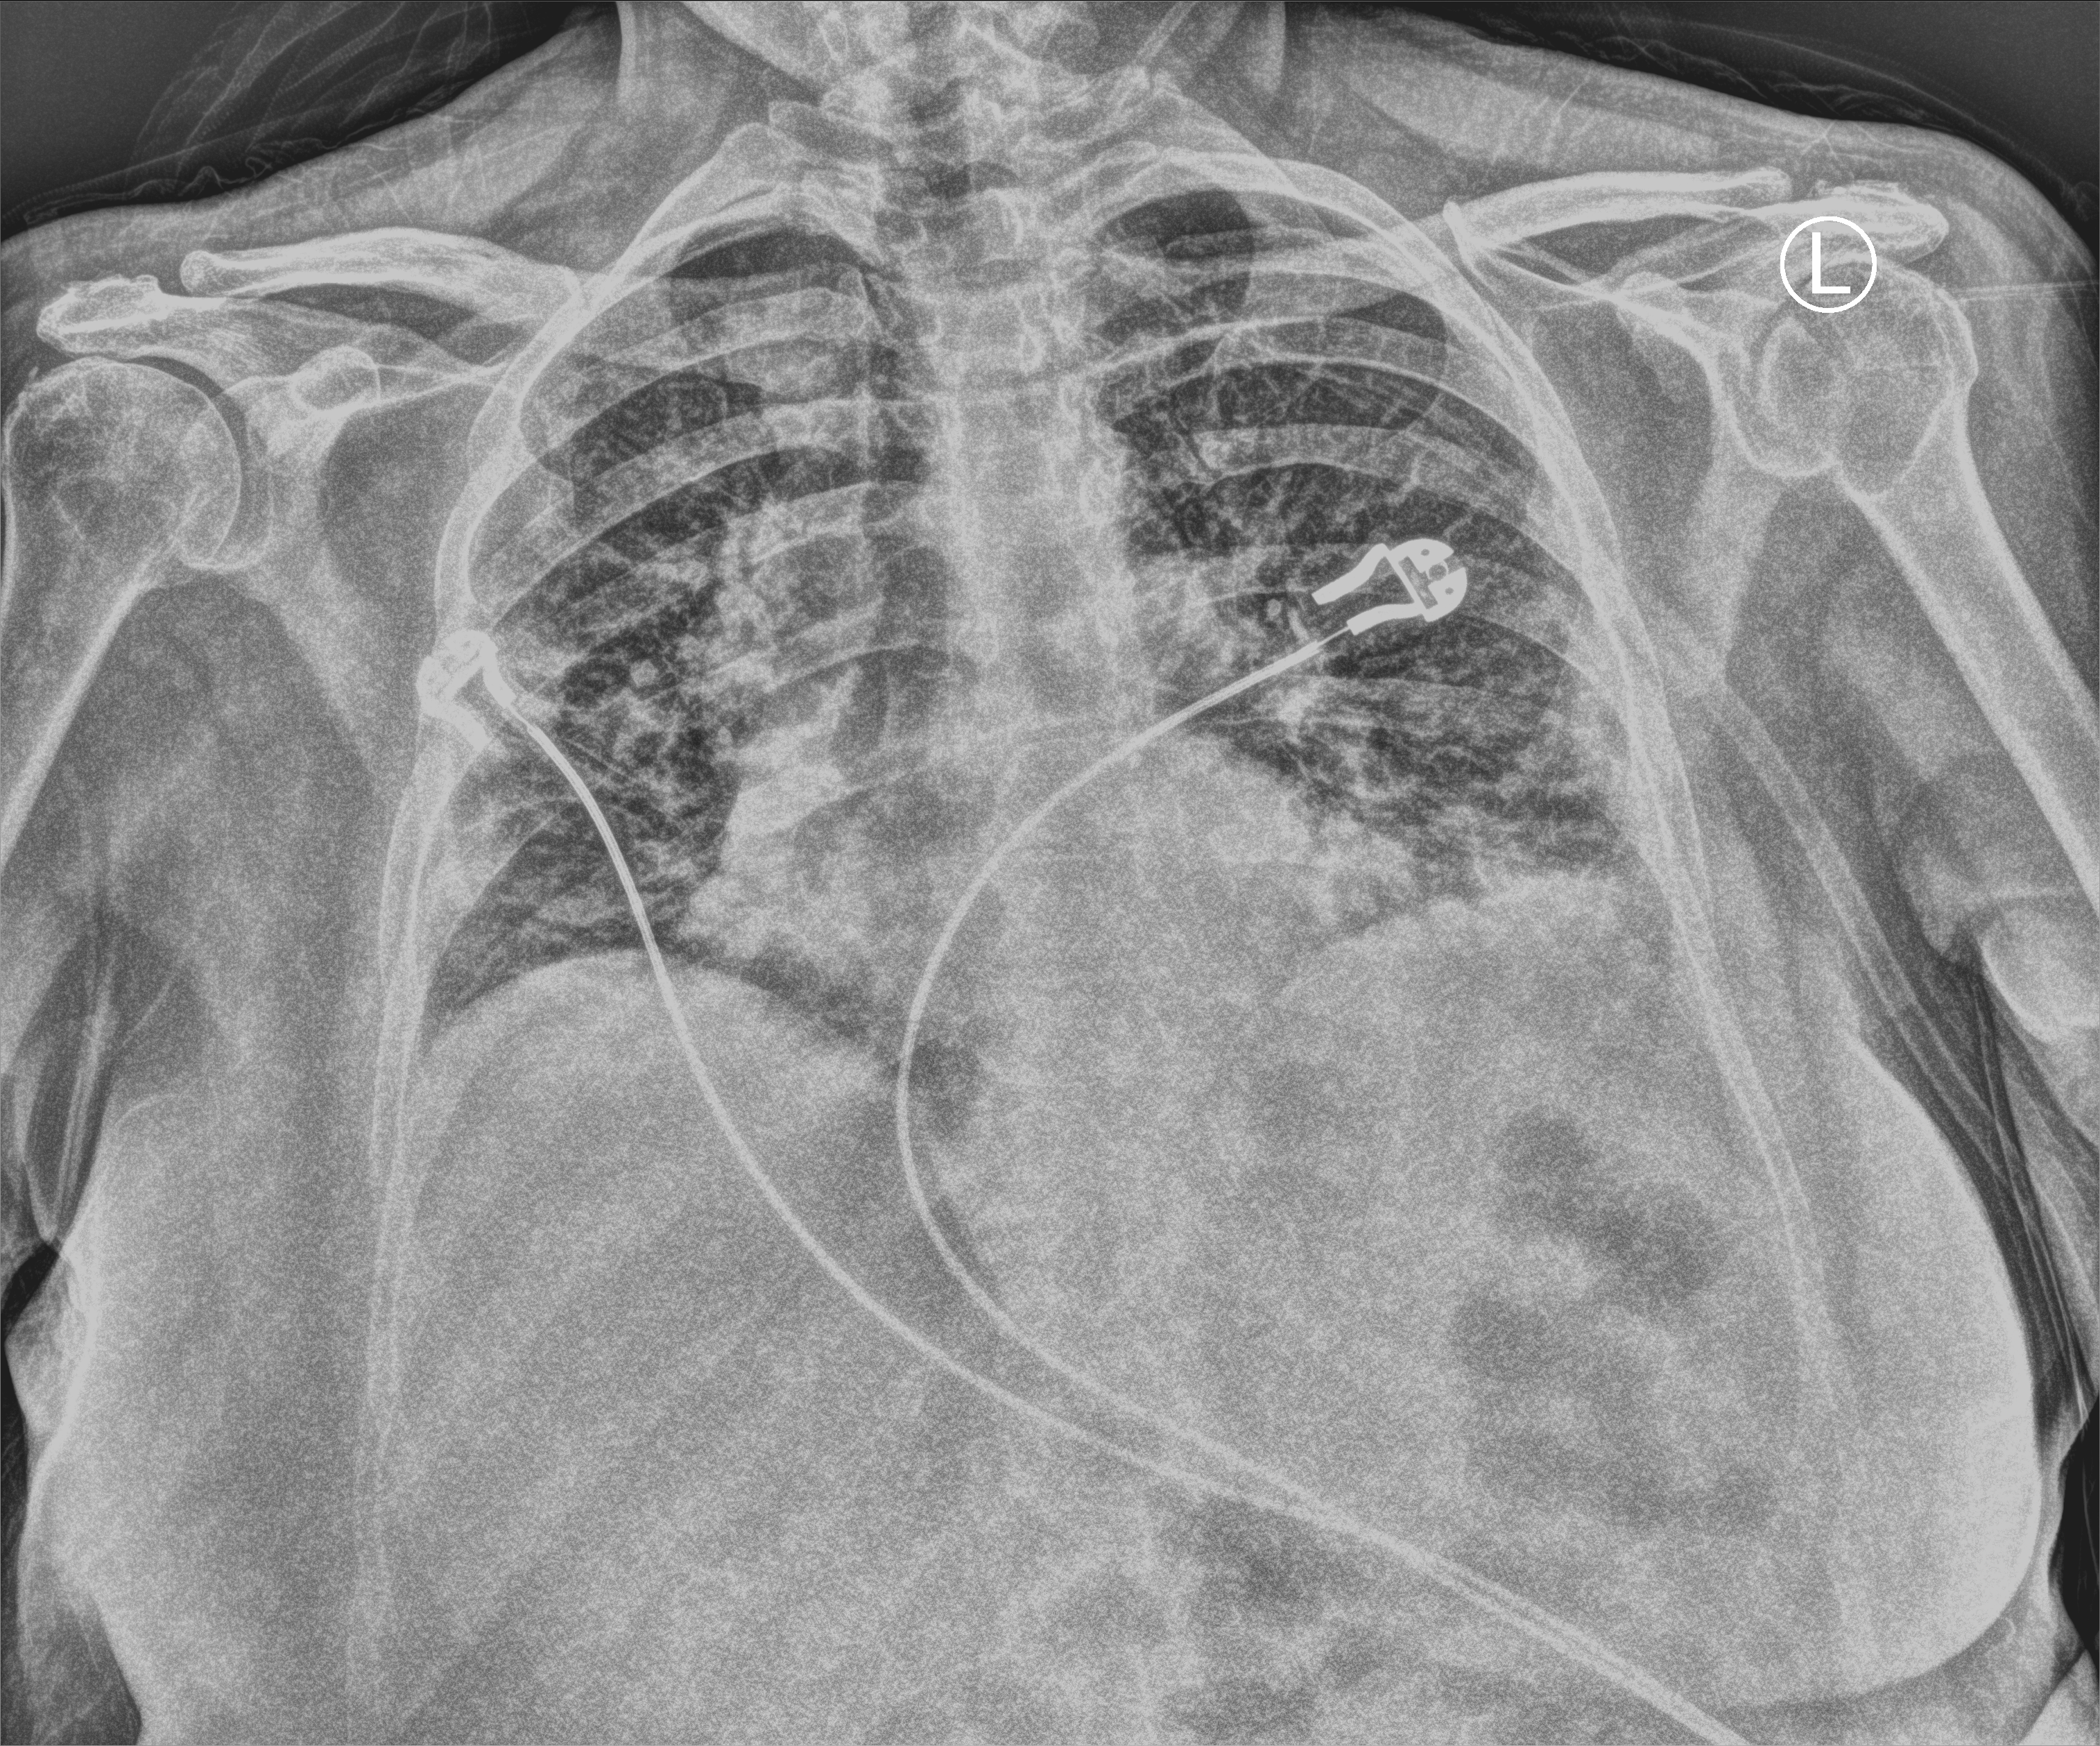
Chest X-ray (portable), anteroposterior (AP) projection. Patient hospitalised with COVID-19; female, aged 60–74 years.
From the hospital-stay record, not from the radiograph (when in the stay this image was taken is not recorded): admitted to intensive care during this hospital stay: no; length of hospital stay: 7 days; mechanically ventilated during this hospital stay: no.